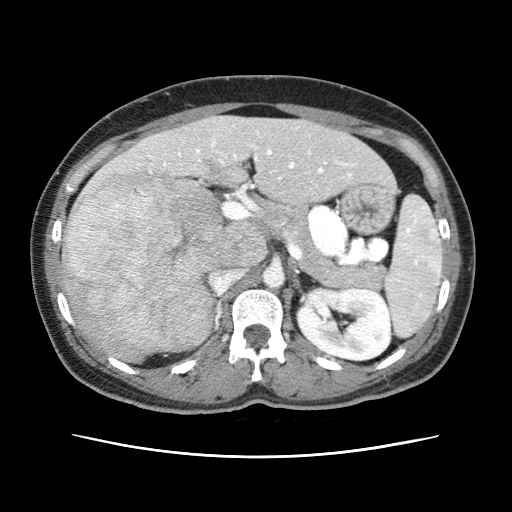
Contrast-enhanced abdominal CT (liver protocol), one axial slice. Slice 29 of 79 in the series (ordered by position). Reconstruction kernel STANDARD. 120 kVp. Soft-tissue window (W 400 / L 40 HU). 2.5 mm slice thickness. 512 × 512 image matrix, field of view 340 × 340 mm. From the clinical record (not read from this slice): diagnosis: hepatocellular carcinoma (patient treated with transarterial chemoembolisation; whether this scan precedes or follows treatment is not stated here); TNM stage (as recorded): Stage-I; Child-Pugh class: A; tumour nodularity: uninodular.
Annotated regions visible in this slice (semi-automatic segmentation, software-assisted and operator-edited):
- abdominal aorta: box from (x=263, y=268) to (x=285, y=288) px
- liver parenchyma outside the tumour (the mass and vessels are separate outlines, so this box may not span the whole liver): (x=62, y=115)–(x=387, y=360)
- mass: (x=62, y=170)–(x=235, y=359)
- liver vessels: (x=163, y=141)–(x=351, y=179)